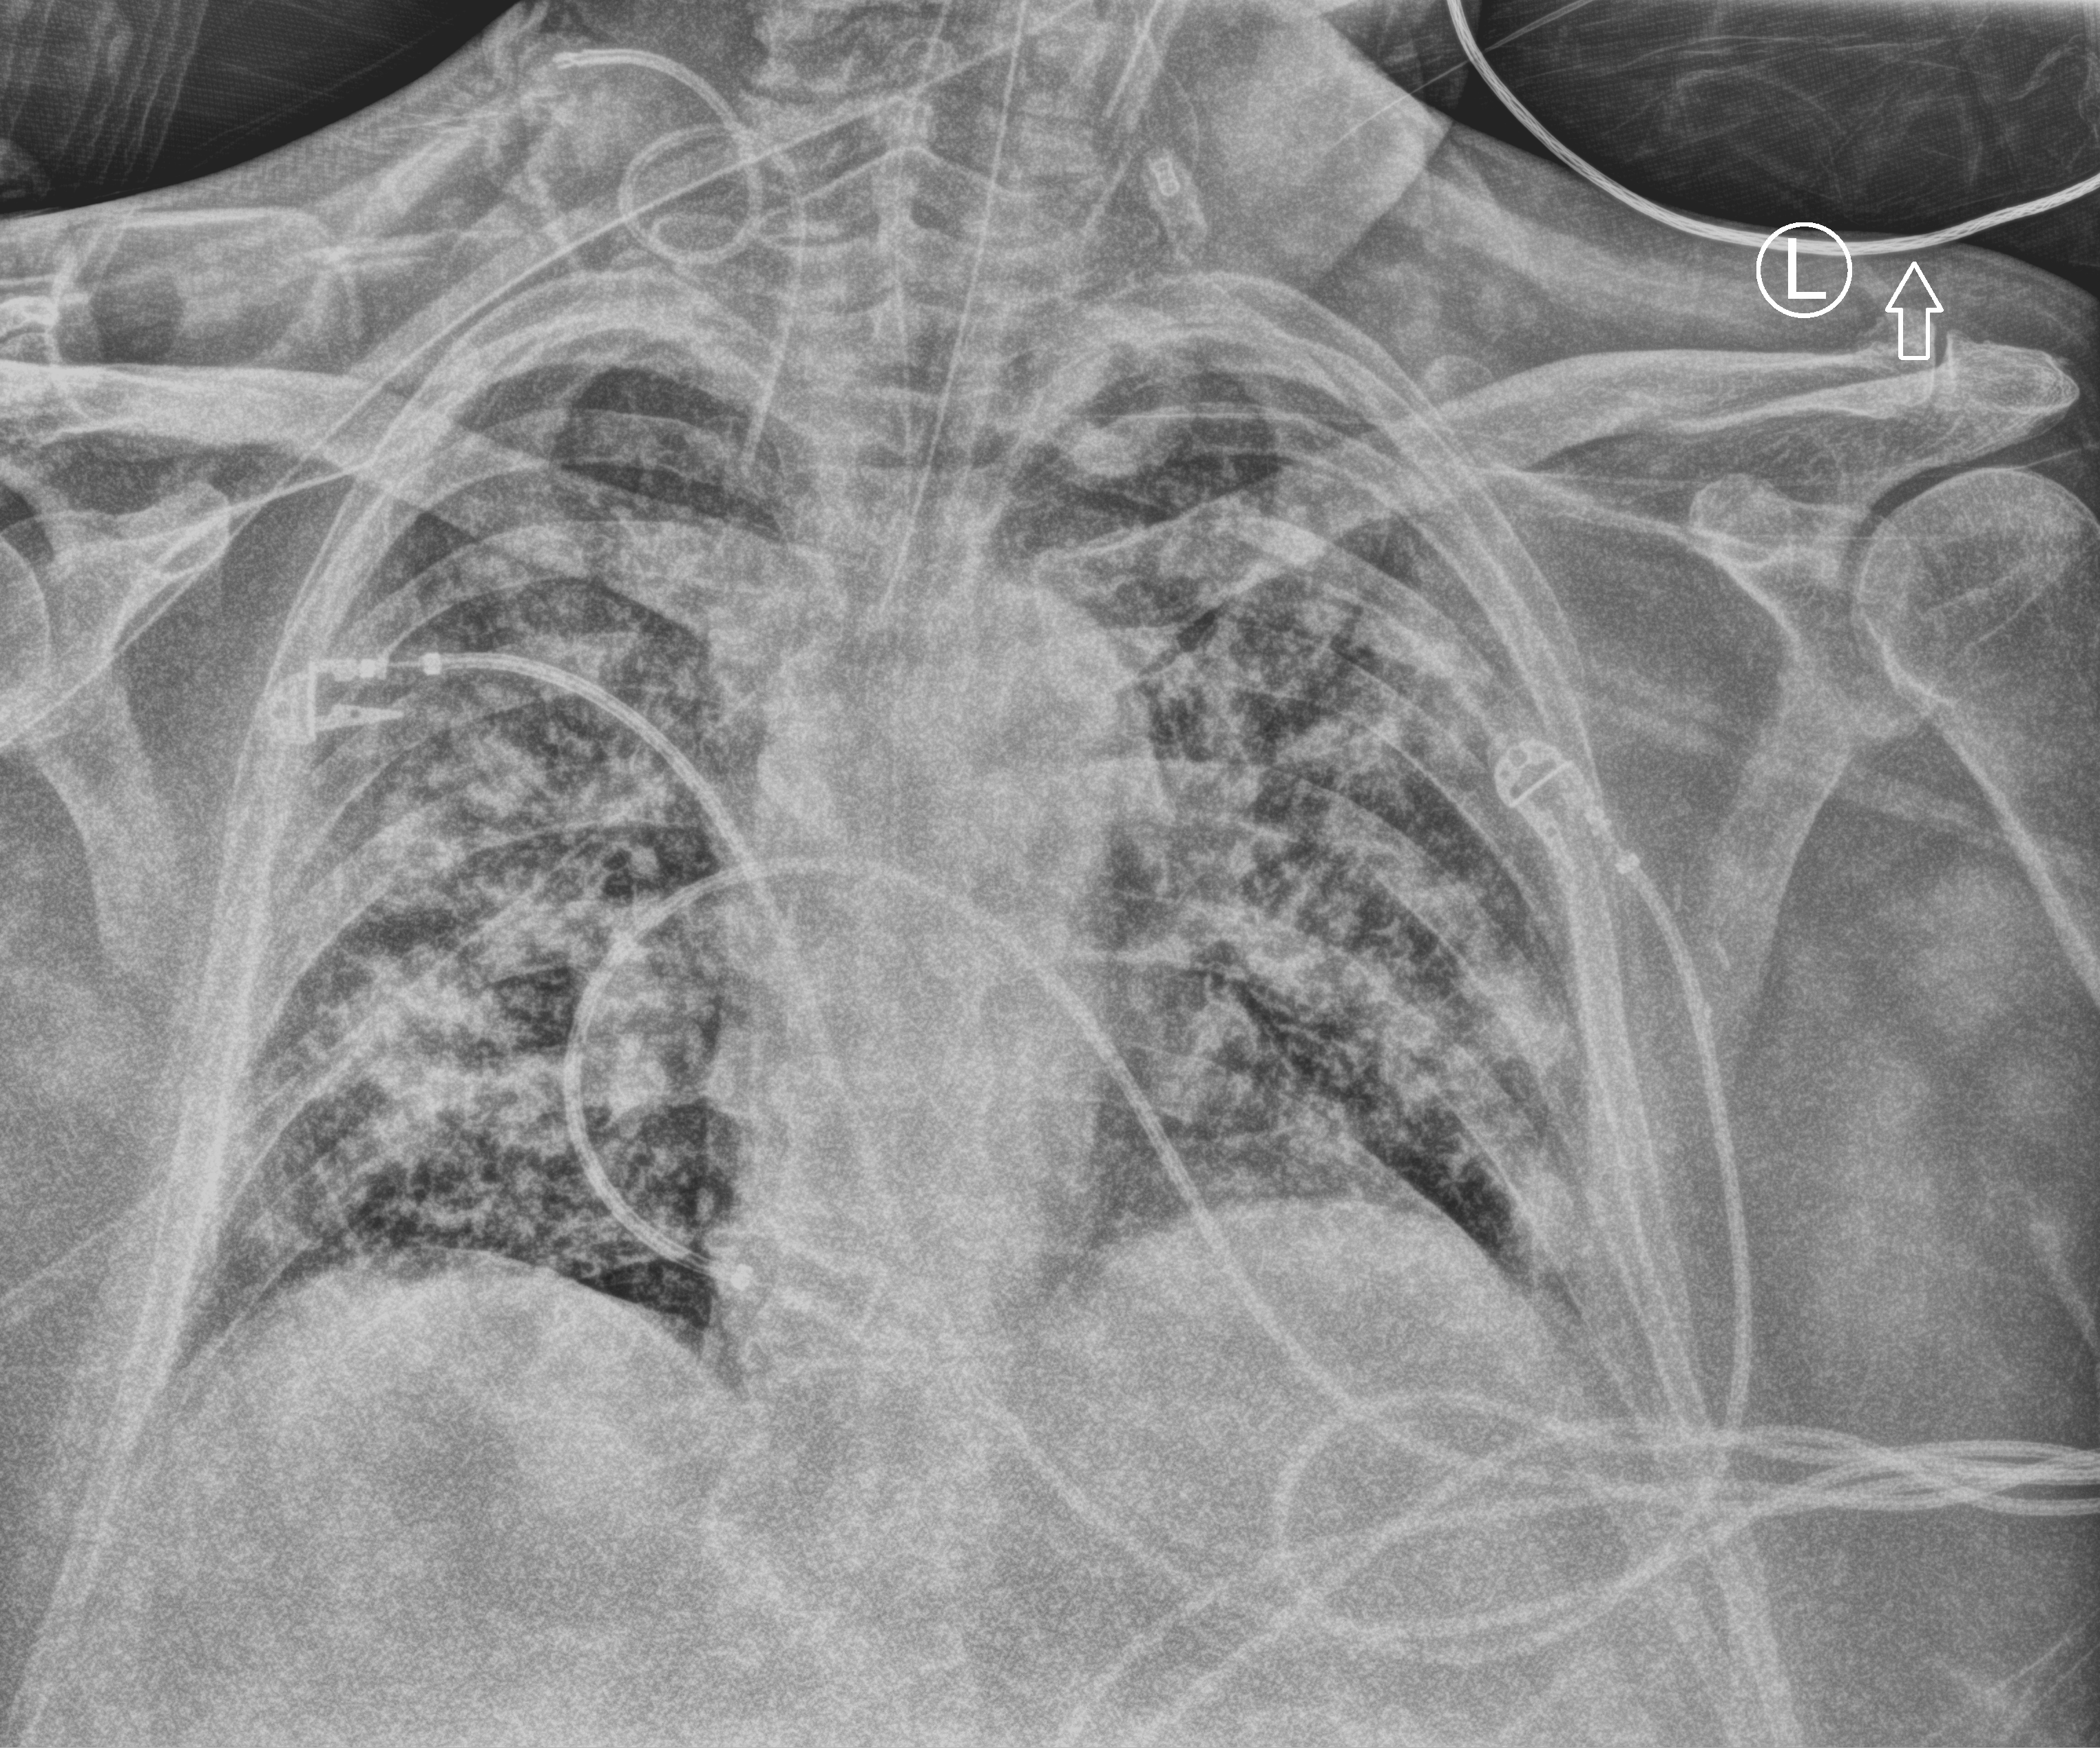
Bedside chest radiograph (computed radiography); anteroposterior (AP) projection. Male patient hospitalised with COVID-19, age 60–74 years.
From the hospital-stay record, not from the radiograph (when in the stay this image was taken is not recorded): mechanically ventilated during this hospital stay: yes; length of hospital stay: 17 days; admitted to intensive care during this hospital stay: yes.